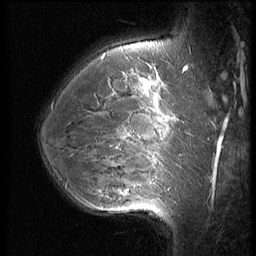
Breast MRI (dynamic contrast-enhanced), one sagittal slice; position 43 of 56 along the scan axis; 3 images stored at this slice position (order not interpretable as contrast timing); 1.5 T; TE 4.2 ms, TR 9 ms; 2.5 mm slice thickness; 256 × 256 image matrix, field of view 180 × 180 mm. Female patient, age 35 years. Case-level facts recorded for this patient, not image findings: setting: breast cancer imaged before/during neoadjuvant chemotherapy; receptor status: HR-positive, HER2-negative.
Outlined on this slice (semi-automatically segmented with operator editing):
- analysis volume of interest (the breast-tissue region the enhancement analysis was run in; not a lesion): bounding box <63,60,190,218> (left, top, right, bottom; pixels)
- tumour enhancement mask (voxels above the 140 % enhancement threshold inside the analysis volume of interest): <114,92,174,192>